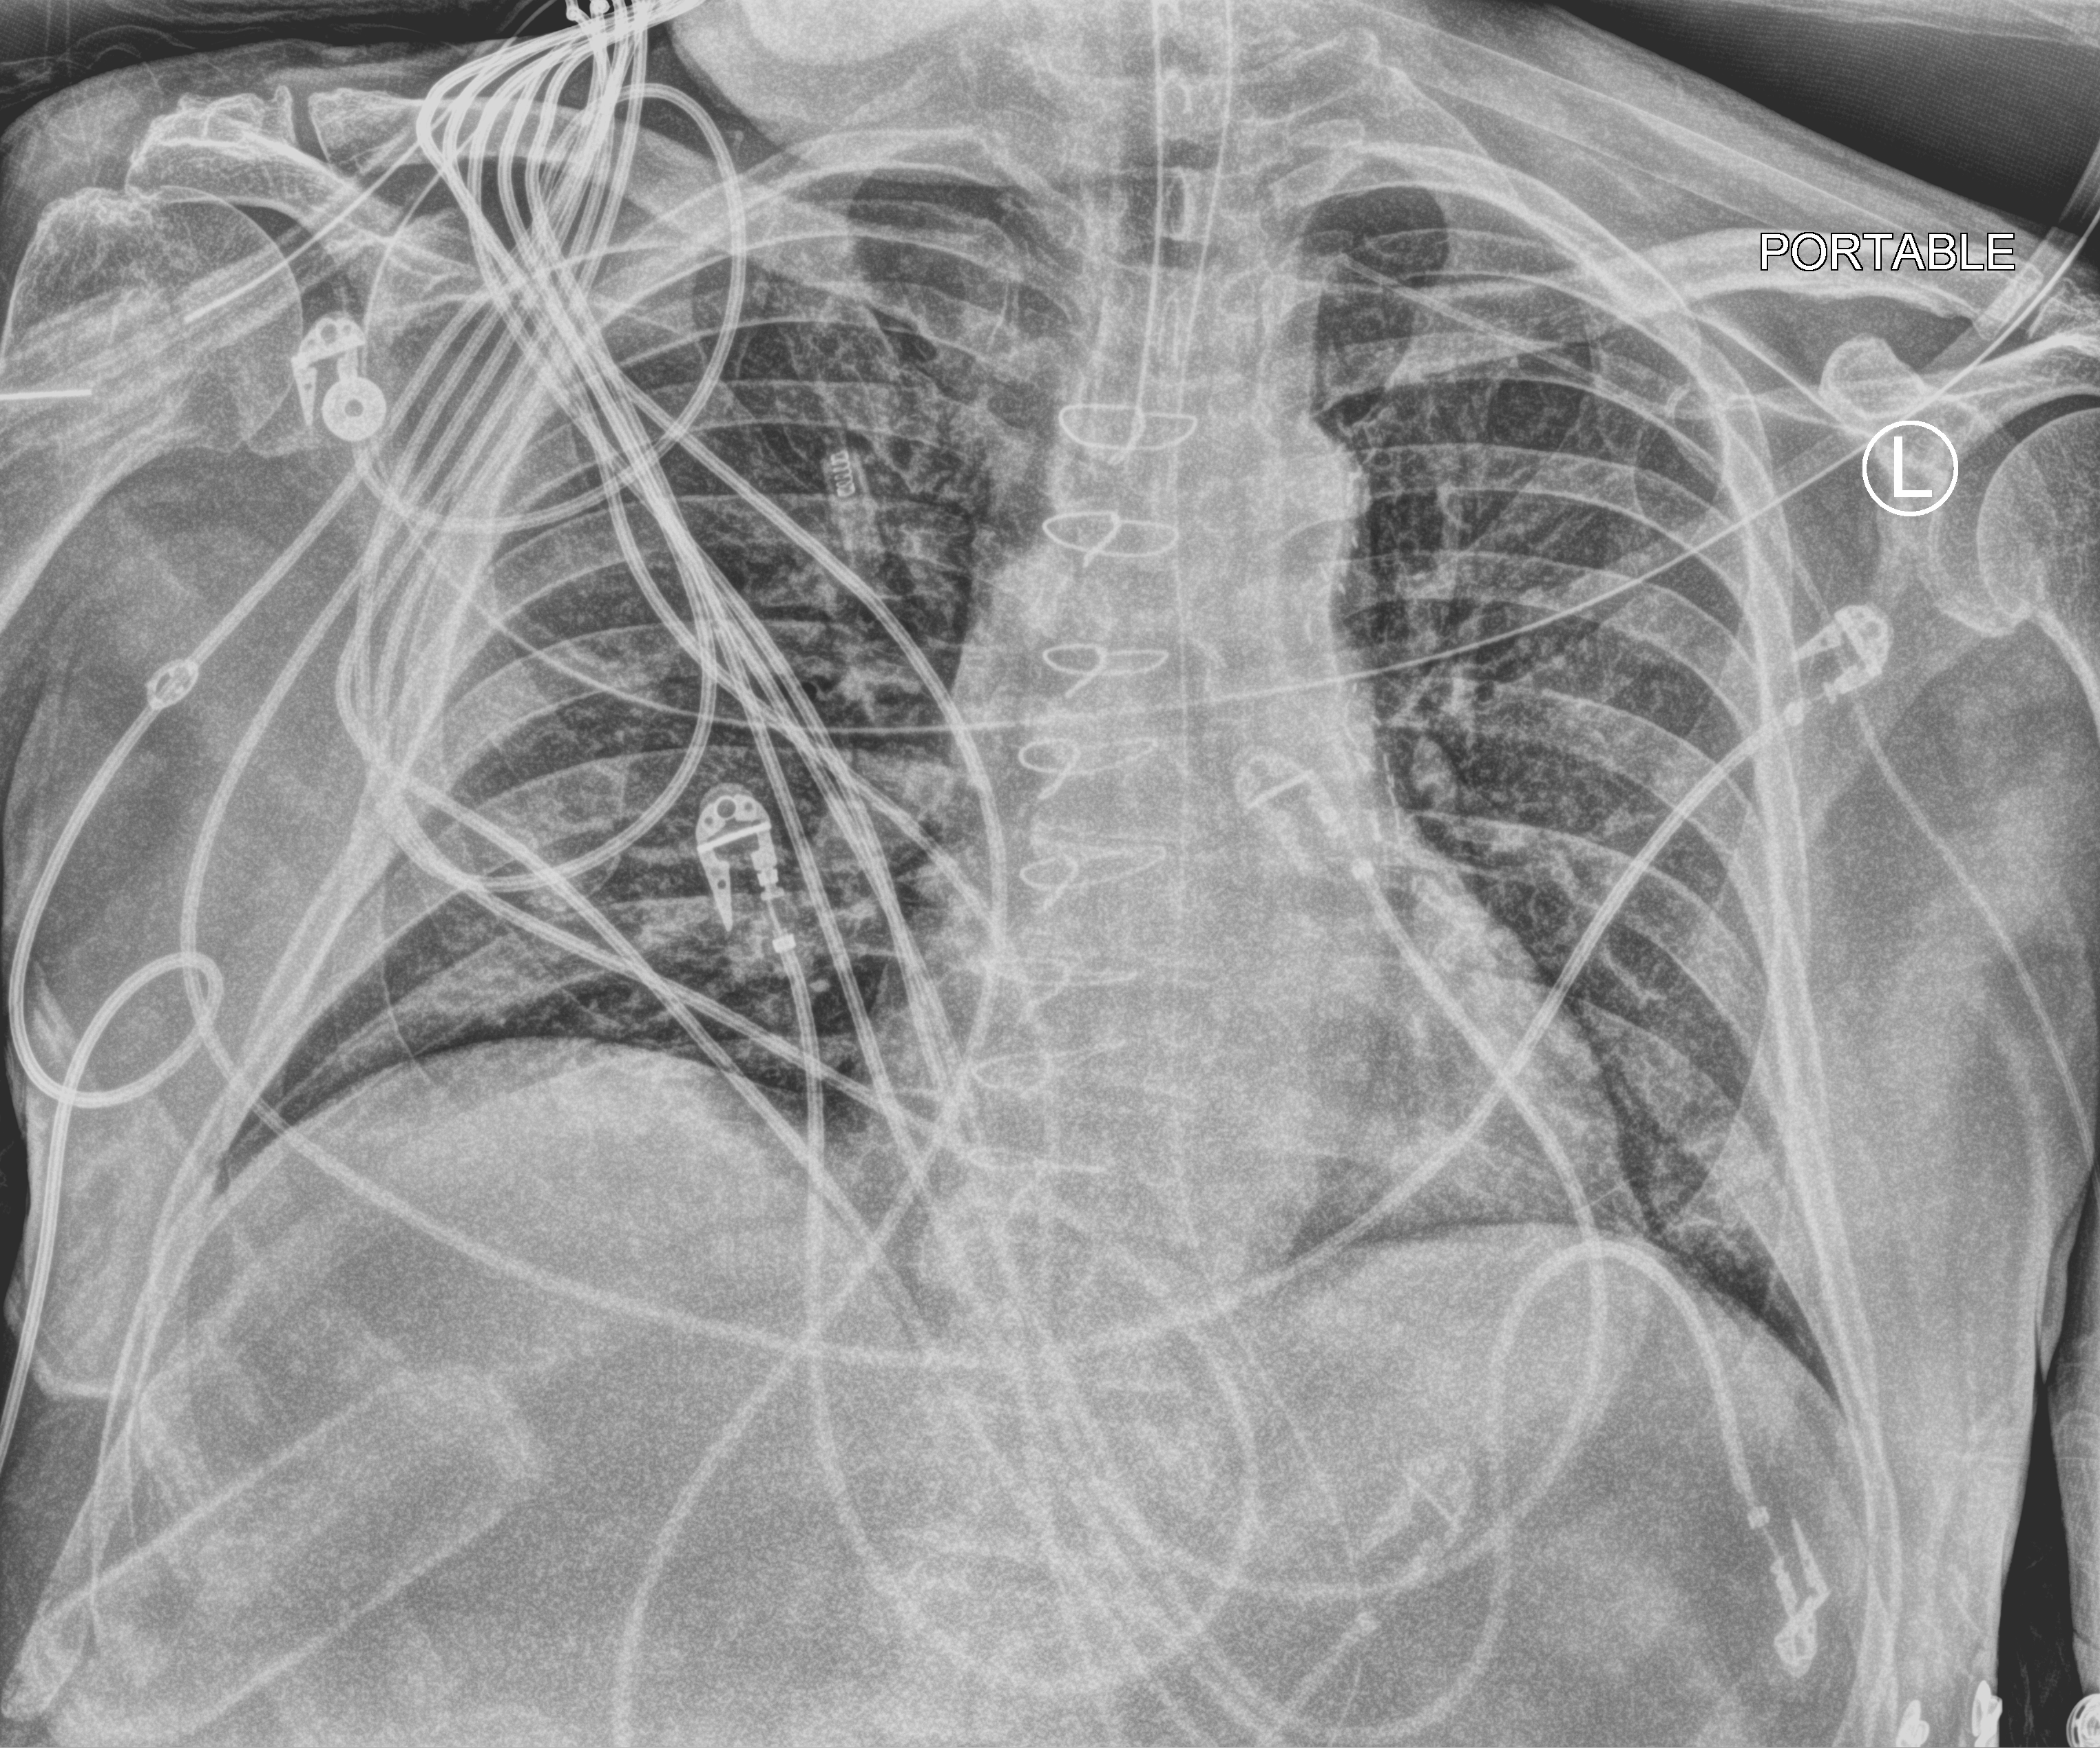
Portable chest radiograph; anteroposterior (AP) projection. Patient hospitalised with COVID-19; male, aged 60–74 years.
From the hospital-stay record, not from the radiograph (when in the stay this image was taken is not recorded):
- admitted to intensive care during this hospital stay: yes